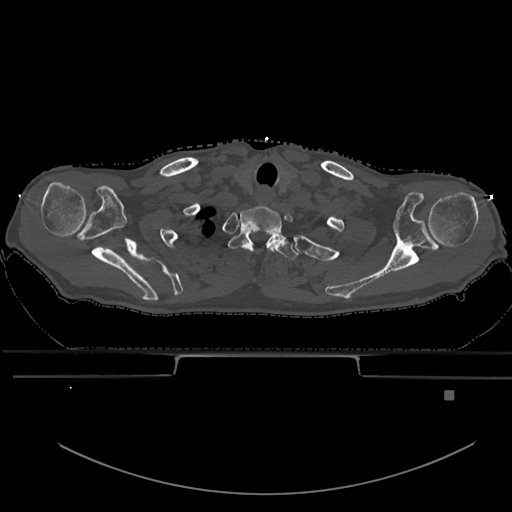
CT including the spine, one axial slice; position 548 of 969 along the scan axis; bone window (W 1800 / L 400 HU); 512 × 512 image matrix, field of view 456 × 456 mm. Patient: male, 82 years. From the clinical record (not read from this slice): primary cancer: prostate.
Structures marked on this image (semi-automatically segmented with operator editing):
- T1 vertebra: bounding box [x1, y1, x2, y2] px = [228, 228, 298, 260]